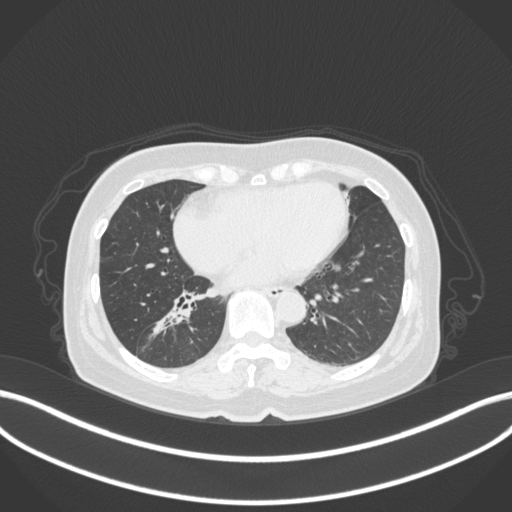
Chest CT, one axial slice. Slice 153 of 429 in the series (ordered by position). Reconstruction kernel B31f. 120 kVp. Lung window (W 1500 / L -600 HU). 1 mm slice thickness. 512 × 512 image matrix, field of view 400 × 400 mm. Female patient, age 67 years. Case-level facts recorded for this patient, not image findings: clinical TNM (as recorded): T1c N1 M0; histopathological grade: G2-3.
Structures marked on this image (rectangle marked by the reading radiologist):
- lung tumour (recorded histology: adenocarcinoma): bounding box [x1, y1, x2, y2] px = [145, 296, 198, 341]